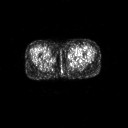
FDG PET of an extremity soft-tissue mass (from a PET/CT study), one axial slice. Slice 3 of 267 in the series (ordered by position). 128 × 128 image matrix. Patient: female, 47 years. Case-level facts recorded for this patient, not image findings: histological type: myxofibrosarcoma; grade: intermediate; site of the primary tumour: left thigh.
Annotated regions visible in this slice (expert contour drawn on MRI and transferred to this co-registered scan by the dataset authors):
- gross tumour volume including surrounding oedema: box from (x=70, y=54) to (x=81, y=60) px